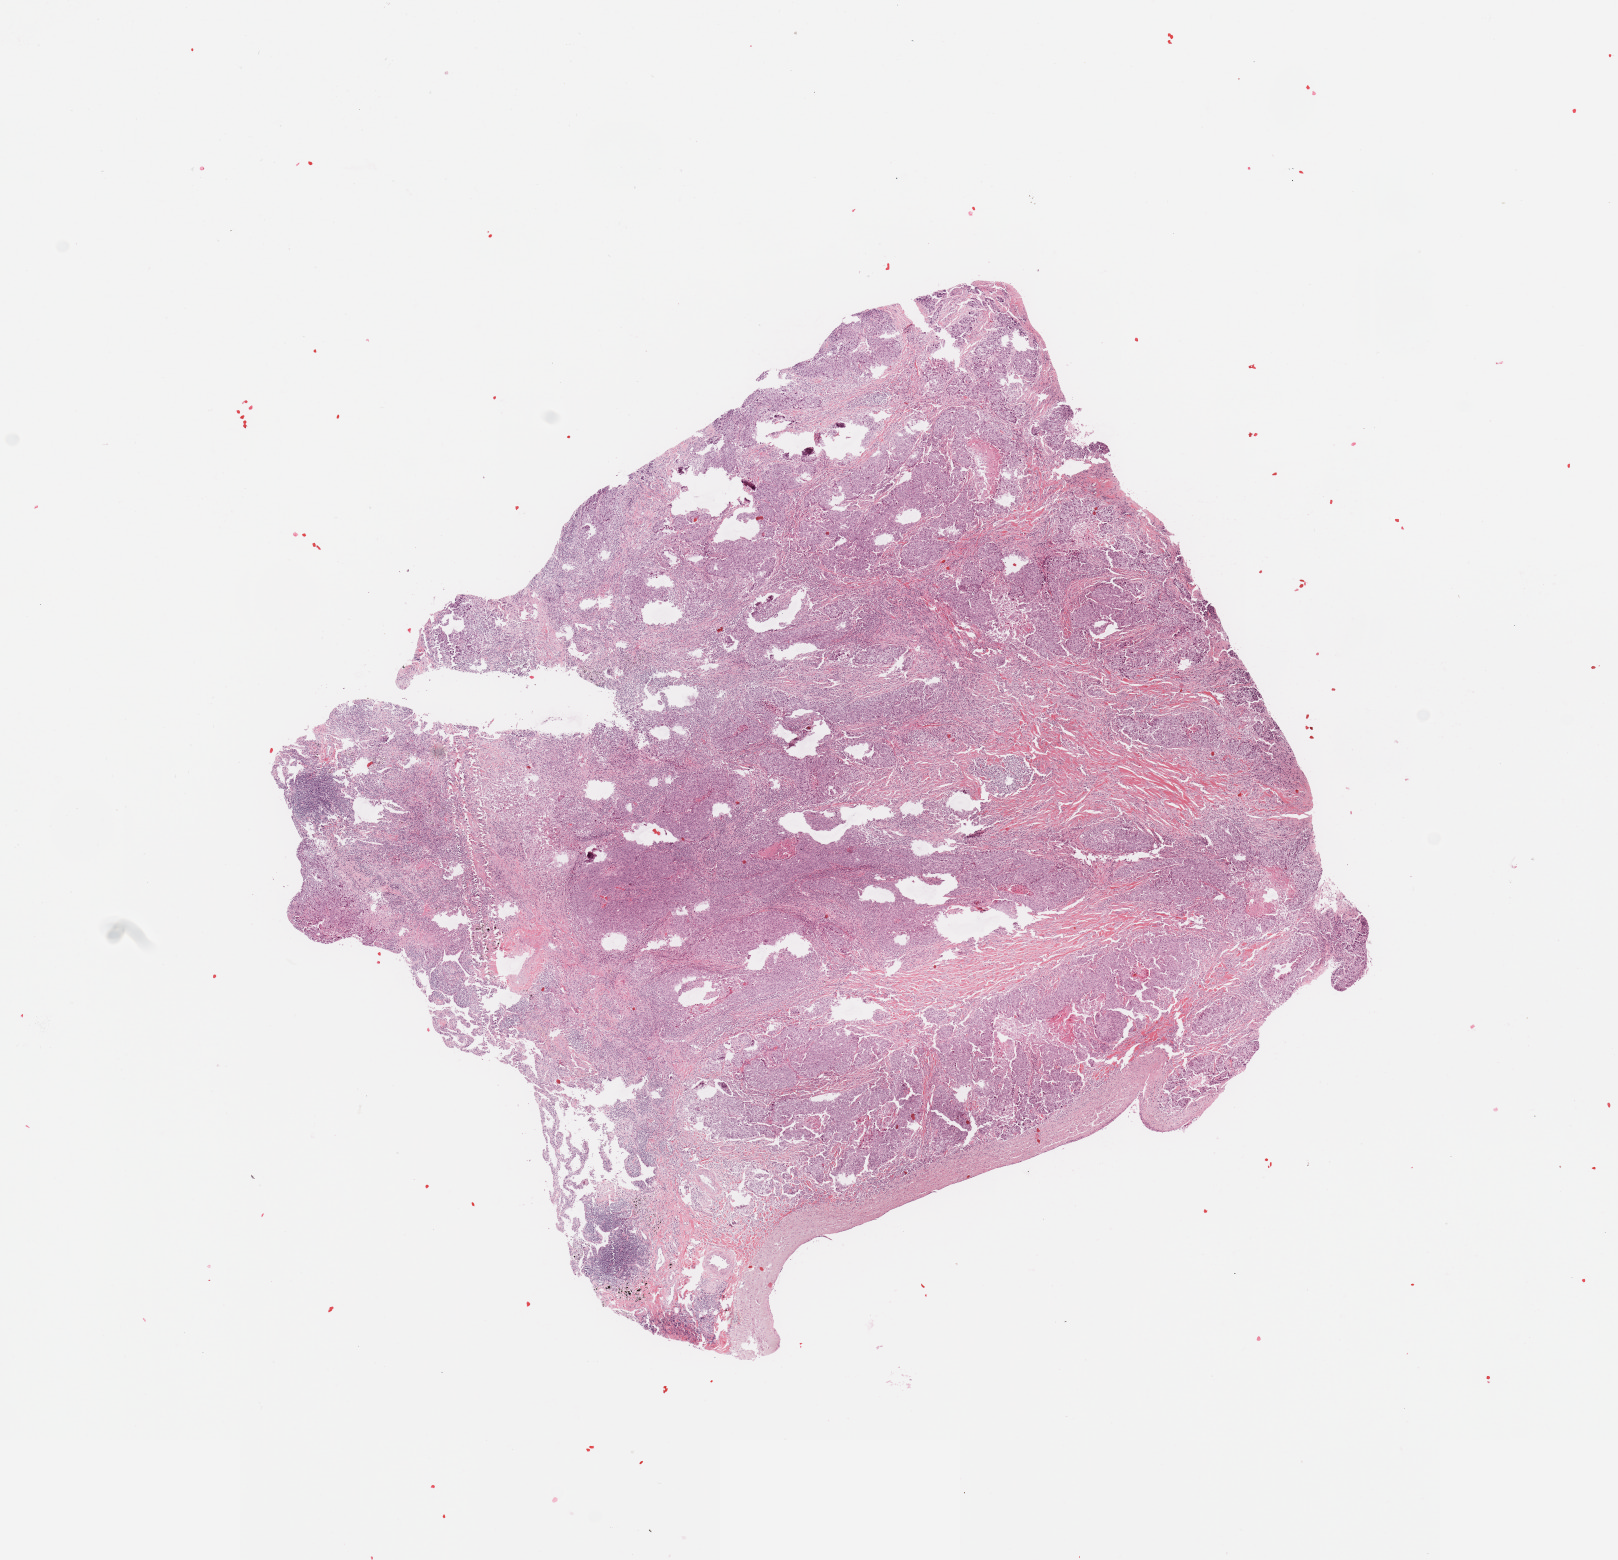
Digitized H&E-stained tissue section (whole slide) — low-resolution overview of the scanned area, about 12.8 x 12.3 mm; tumour tissue sample, sampled site: lung. Patient: male, age 76 years. Histologic grade: G2 (moderately differentiated). Pathologist review of this section (percent, as recorded): tumour nuclei 75%, necrosis 3%.
Primary tumour site (as recorded): left upper lobe. Diagnosis: Squamous cell carcinoma, NOS. AJCC pathologic stage: IIB.